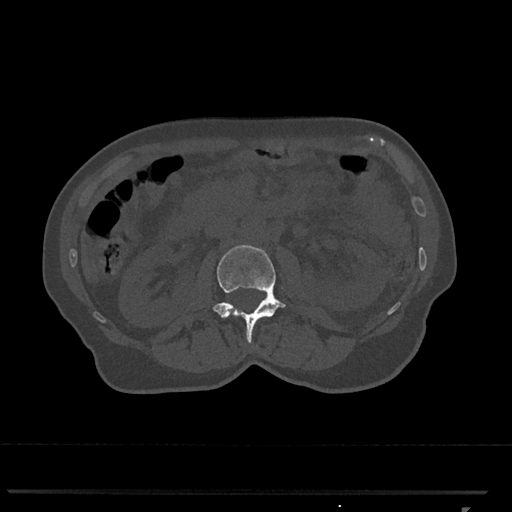
CT including the spine, one axial slice; position 336 of 793 along the scan axis; bone window (W 1800 / L 400 HU); 0.5 mm slice thickness; 512 × 512 image matrix. Patient: female, 62 years. From the clinical record (not read from this slice): primary cancer: renal.
Outlined on this slice (semi-automatically segmented with operator editing):
- L2 vertebra: bounding box [x1, y1, x2, y2] px = [212, 245, 286, 343]